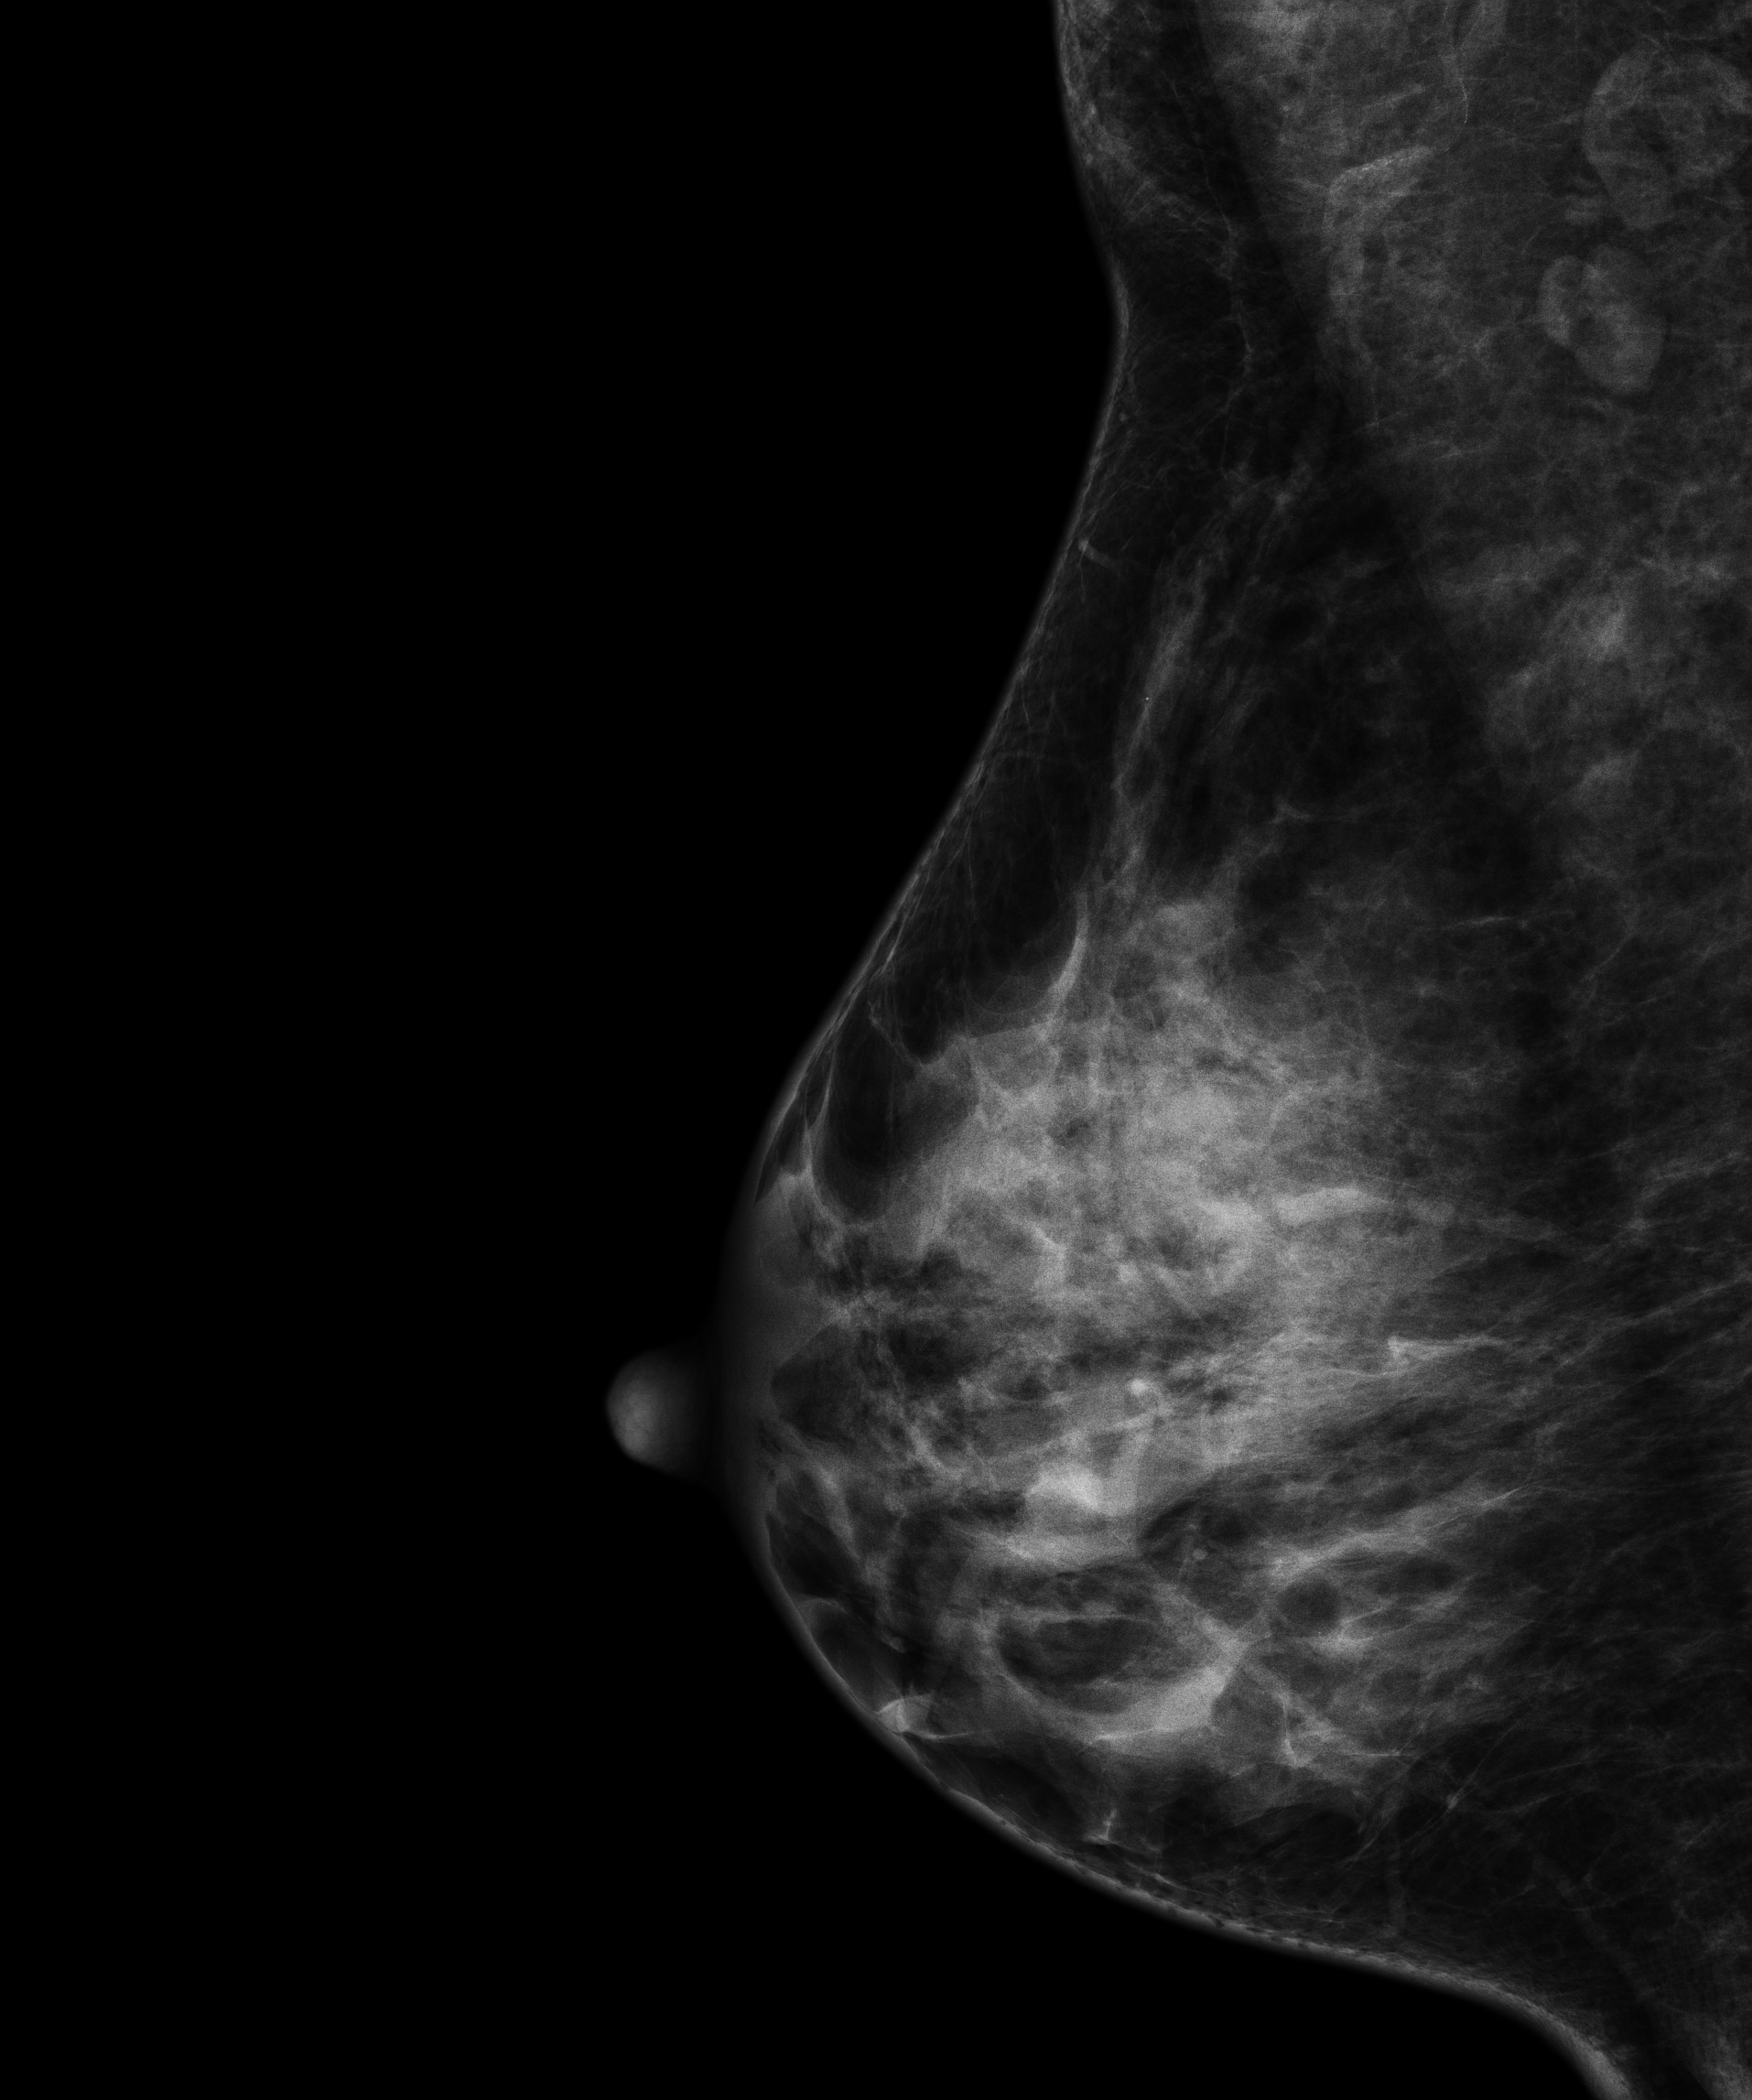
Full-field digital mammogram (FFDM), right breast, MLO view, screening examination. Patient aged 55 years (female).
BI-RADS breast density category at the screening exam (both breasts, scale 1–4): 3. Final BI-RADS category for the screening round (tomosynthesis exam, both breasts): category 1. Recall: no recall after this screen.